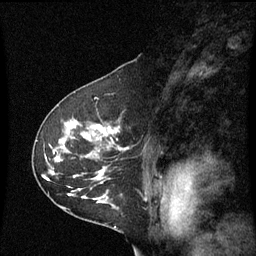
Breast MRI (dynamic contrast-enhanced), one sagittal slice; position 40 of 60 along the scan axis; dynamic contrast-enhanced series, image 2 of 3 at this slice position (ordered by acquisition); 1.5 T; TE 4.2 ms, TR 8.9 ms; 2 mm slice thickness; 256 × 256 image matrix. Patient: female, 53 years. From the clinical record (not read from this slice): setting: breast cancer imaged before/during neoadjuvant chemotherapy; receptor status: HR-positive, HER2-negative.
Structures marked on this image (semi-automatically segmented with operator editing):
- analysis volume of interest (the breast-tissue region the enhancement analysis was run in; not a lesion): bounding box <34,100,131,221> (left, top, right, bottom; pixels)
- tumour enhancement mask (voxels above the 70 % enhancement threshold inside the analysis volume of interest): <100,126,119,175>